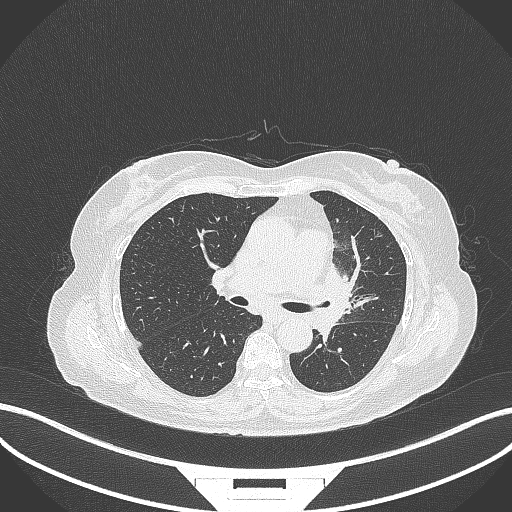
Chest CT, one axial slice; slice 195 of 382 in the series (ordered by position); reconstruction kernel B70f; 120 kVp; lung window (W 1500 / L -600 HU); 1 mm slice thickness; 512 × 512 image matrix, field of view 400 × 400 mm. Patient: female, 64 years. From the clinical record (not read from this slice): clinical TNM (as recorded): T2a N2 M0.
Outlined on this slice (rectangle marked by the reading radiologist):
- lung tumour (recorded histology: adenocarcinoma): bounding box [x1, y1, x2, y2] px = [319, 256, 357, 335]